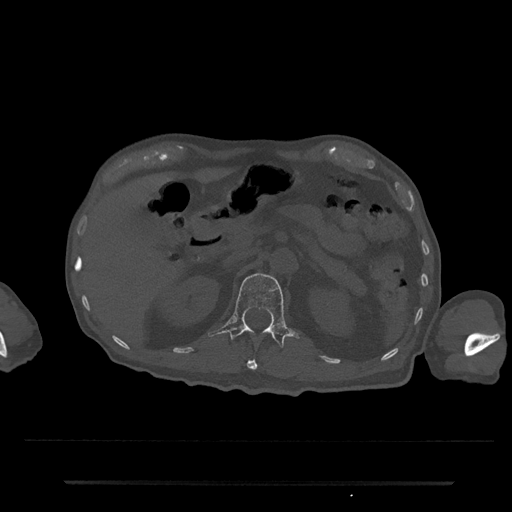
CT including the spine, one axial slice. Slice 144 of 797 in the series (ordered by position). Reconstruction kernel Br40s/3. 120 kVp. Bone window (W 1800 / L 400 HU). 0.5 mm slice thickness. 512 × 512 image matrix, field of view 427 × 427 mm. Male patient, age 74 years. From the clinical record (not read from this slice): primary cancer: prostate.
Structures marked on this image (semi-automatically segmented with operator editing):
- L1 vertebra: bounding box [x1, y1, x2, y2] px = [209, 273, 298, 349]
- T12 vertebra: [247, 358, 258, 370]